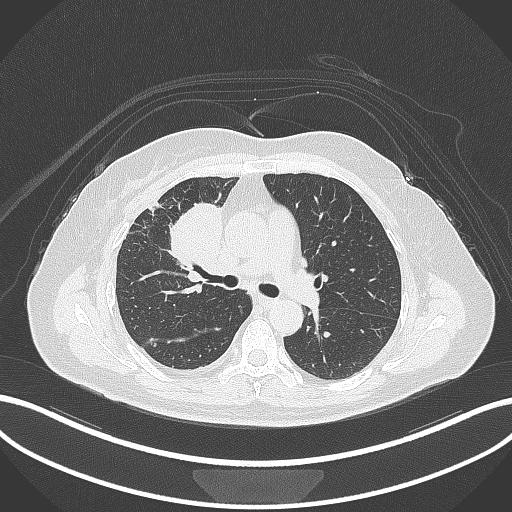
Chest CT, one axial slice; slice 171 of 305 in the series (ordered by position); lung window (W 1500 / L -600 HU); 1 mm slice thickness; 512 × 512 image matrix, field of view 400 × 400 mm. Female patient, age 52 years. From the clinical record (not read from this slice): clinical TNM (as recorded): T3 N1 M1.
Structures marked on this image (bounding box drawn by a radiologist):
- lung tumour (recorded histology: adenocarcinoma): box from (x=158, y=197) to (x=226, y=280) px